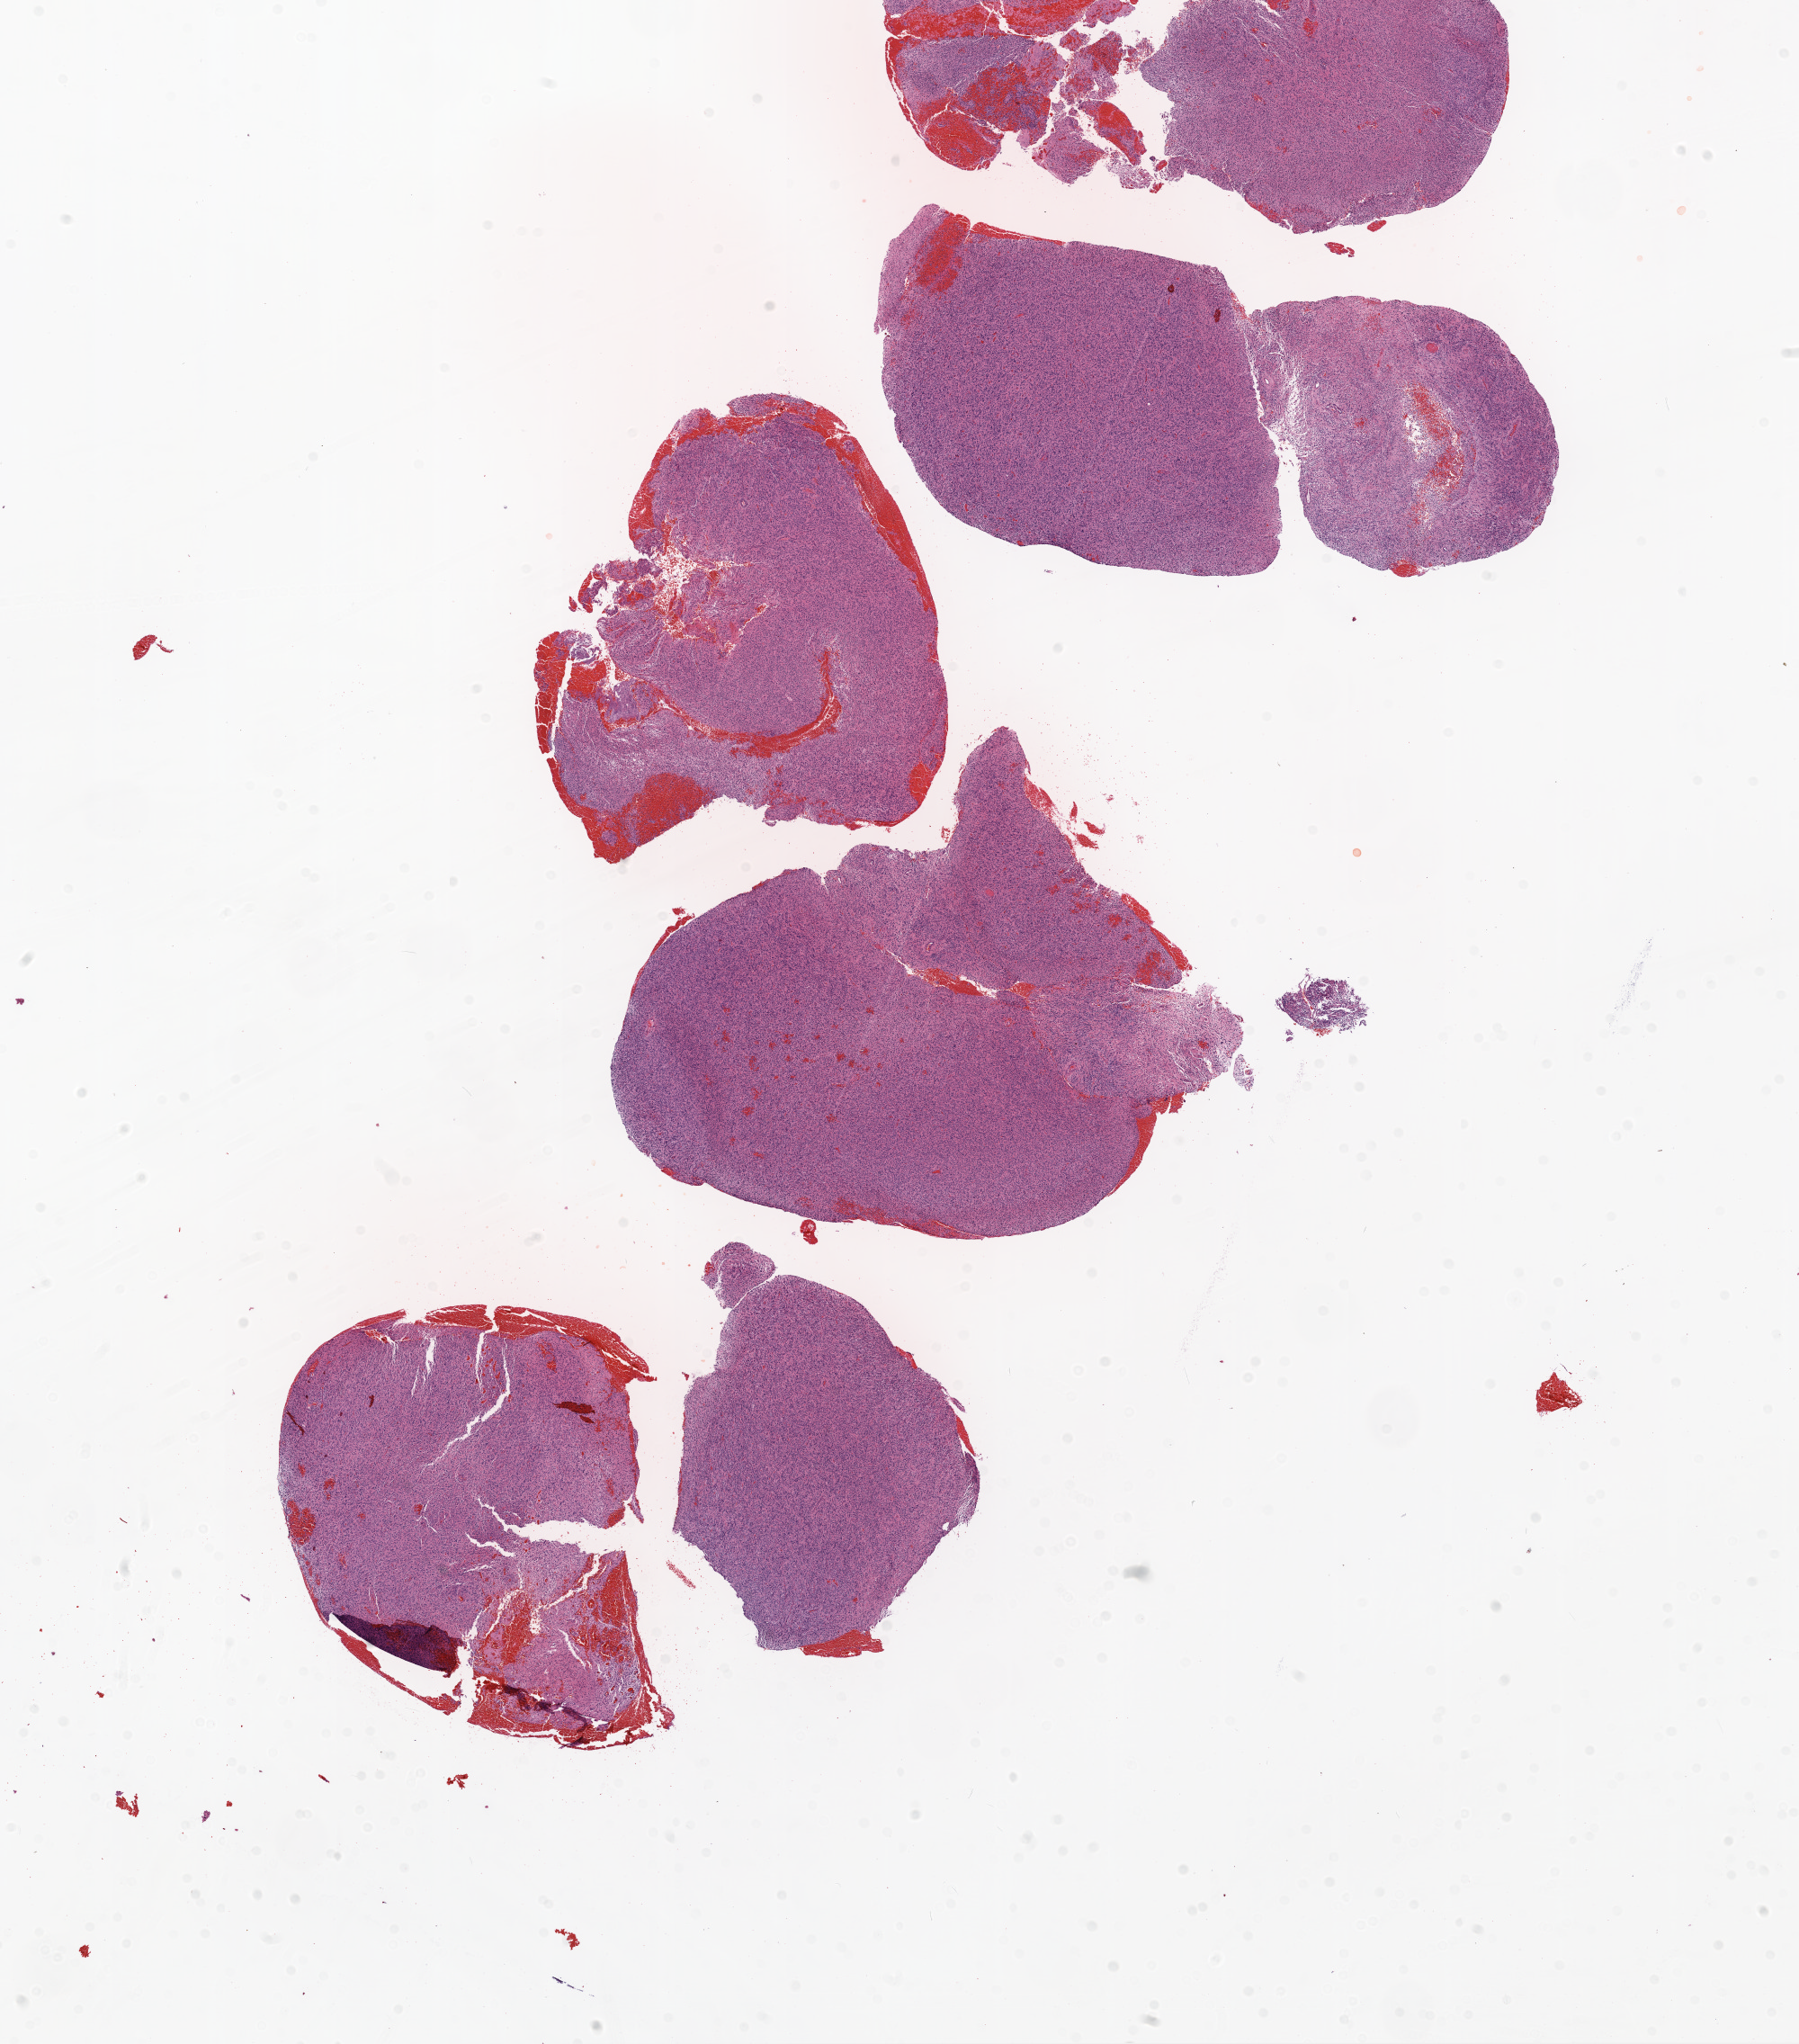
H&E-stained whole-slide image — whole scanned area (about 16.0 x 18.2 mm) shown as a low-resolution overview; formalin-fixed paraffin-embedded (FFPE) diagnostic section; sample: primary tumour, brain. Patient: male, age at initial diagnosis 53 years.
Diagnosis: Glioblastoma.